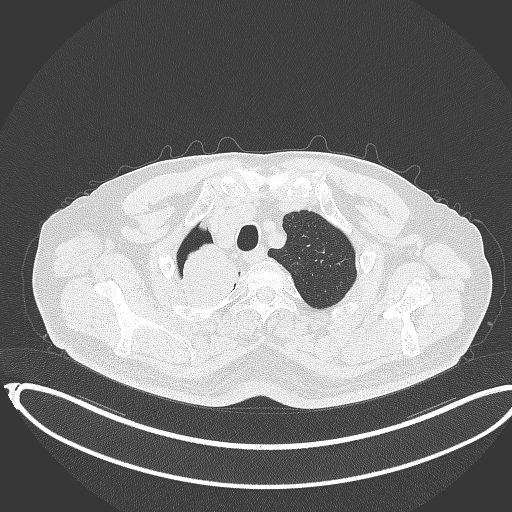
Chest CT, one axial slice. Slice 326 of 403 in the series (ordered by position). Reconstruction kernel B70f. 120 kVp. Lung window (W 1500 / L -600 HU). 1 mm slice thickness. 512 × 512 image matrix, field of view 436 × 436 mm. Male patient, age 68 years. From the clinical record (not read from this slice): clinical TNM (as recorded): T2a N0 M0.
Outlined on this slice (bounding box drawn by a radiologist):
- lung tumour (recorded histology: adenocarcinoma): bounding box <173,241,244,316> (left, top, right, bottom; pixels)